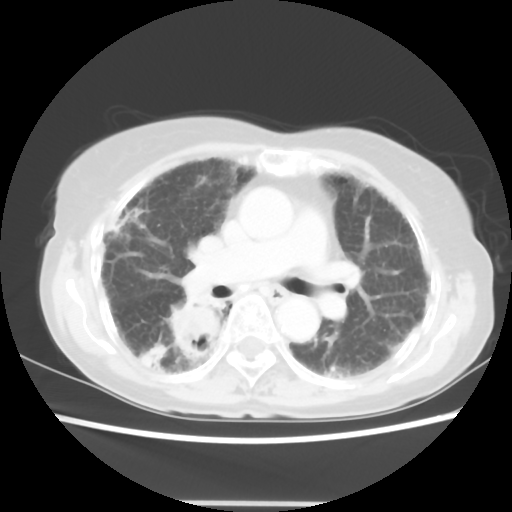
Chest CT, one axial slice; slice 31 of 52 in the series (ordered by position); reconstruction kernel STANDARD; 120 kVp; lung window (W 1500 / L -600 HU); 512 × 512 image matrix. Patient: female, 71 years. From the clinical record (not read from this slice): clinical TNM (as recorded): T3 N0 M0.
Annotated regions visible in this slice (bounding box drawn by a radiologist):
- lung tumour (recorded histology: squamous cell carcinoma): bounding box <166,299,228,376> (left, top, right, bottom; pixels)